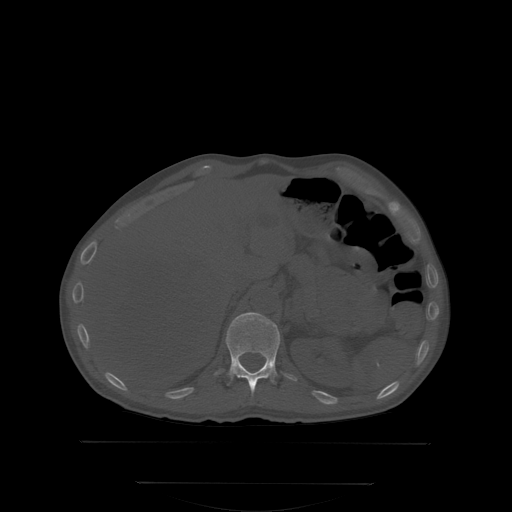
CT including the spine, one axial slice; slice 167 of 350 in the series (ordered by position); bone window (W 1800 / L 400 HU); 2.5 mm slice thickness; 512 × 512 image matrix. Patient: male, 58 years. Case-level facts recorded for this patient, not image findings: primary cancer: prostate.
Structures marked on this image (semi-automatically segmented with operator editing):
- T12 vertebra: box from (x=226, y=313) to (x=281, y=397) px